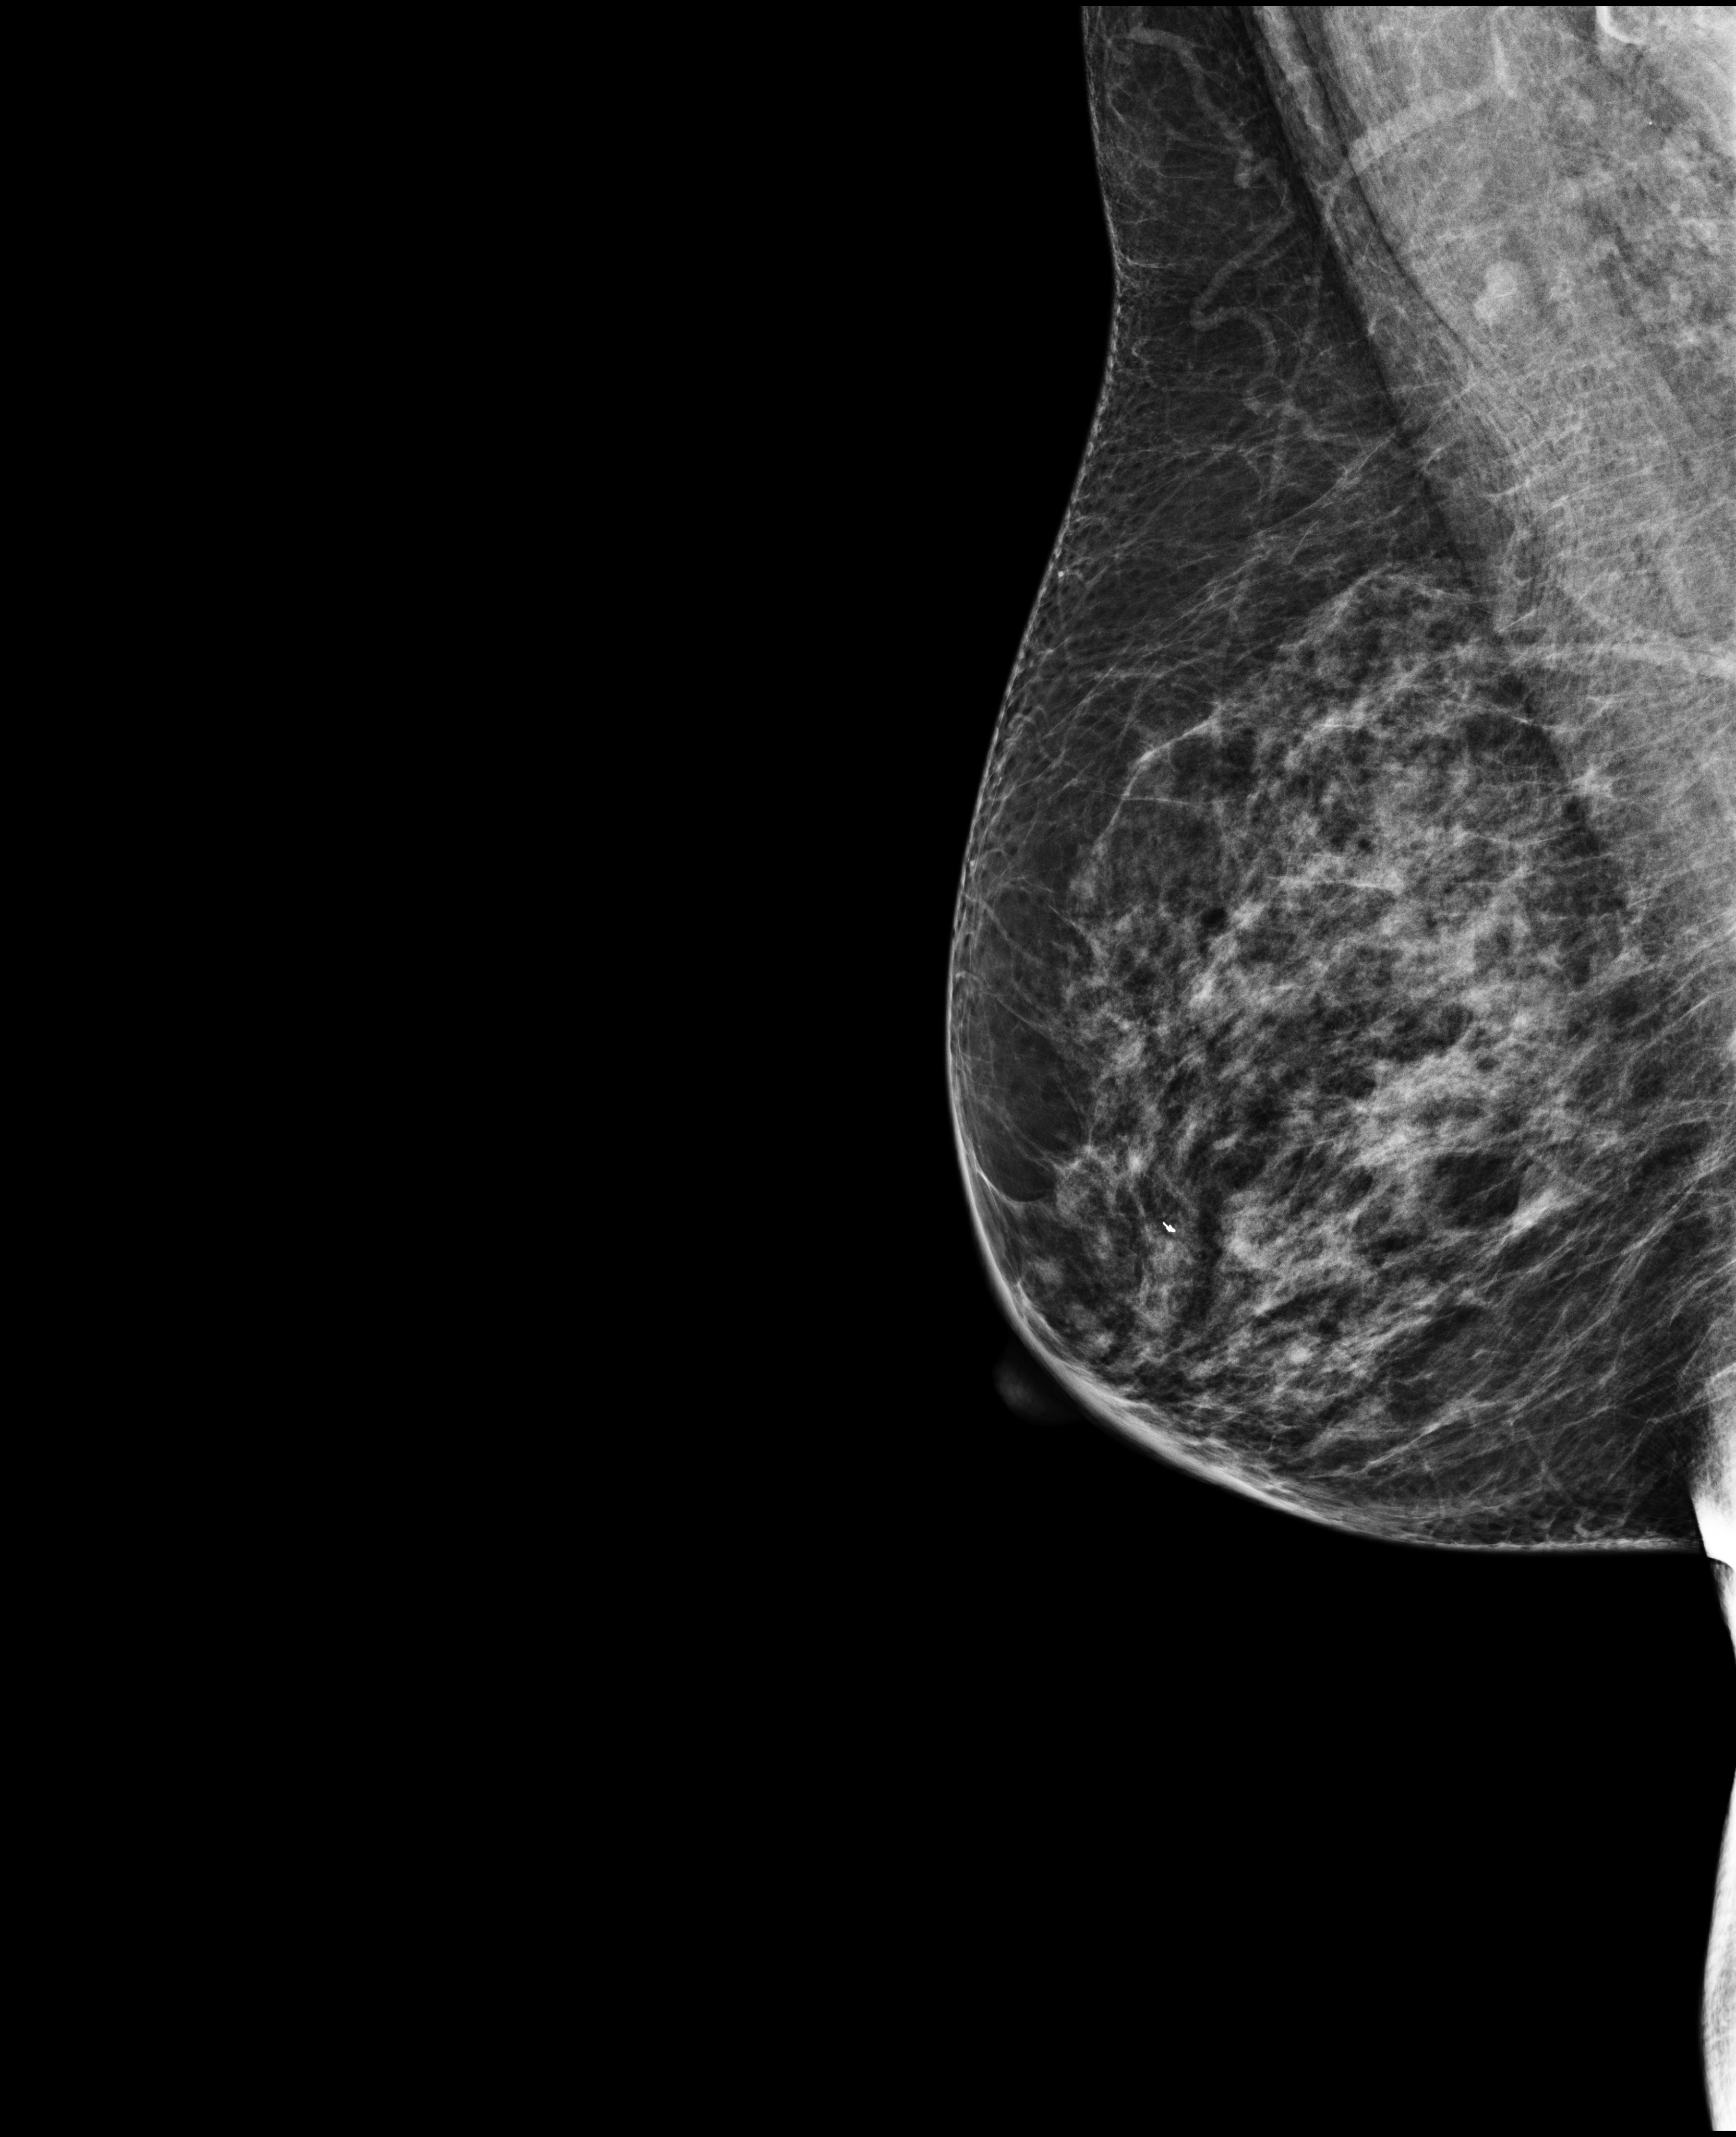
Annual screening mammography examination, system: Selenia Dimensions.
Image type: full-field digital mammogram. Breast: right. Projection: medio-lateral oblique projection.